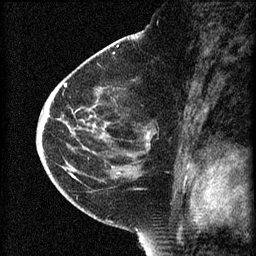
Breast MRI (dynamic contrast-enhanced), one sagittal slice; 3 images stored at this slice position (order not interpretable as contrast timing); 1.5 T; TE 4.2 ms, TR 8.2 ms; 256 × 256 image matrix. Female patient, age 44 years.
Outlined on this slice (semi-automatically segmented with operator editing):
- analysis volume of interest (the breast-tissue region the enhancement analysis was run in; not a lesion): bounding box <73,86,159,165> (left, top, right, bottom; pixels)
- tumour enhancement mask (voxels above the 70 % enhancement threshold inside the analysis volume of interest): <148,134,150,139>